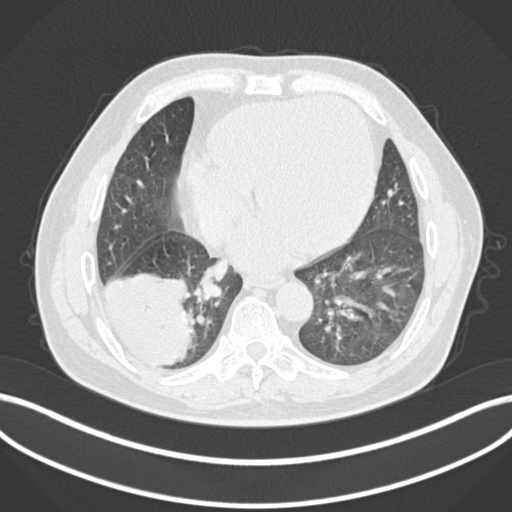
Chest CT, one axial slice; position 50 of 200 along the scan axis; reconstruction kernel B30f; lung window (W 1500 / L -600 HU); 1 mm slice thickness; 512 × 512 image matrix, field of view 400 × 400 mm. Male patient, age 59 years.
Structures marked on this image (rectangle marked by the reading radiologist):
- lung tumour (recorded histology: adenocarcinoma): bounding box [x1, y1, x2, y2] px = [102, 268, 192, 371]